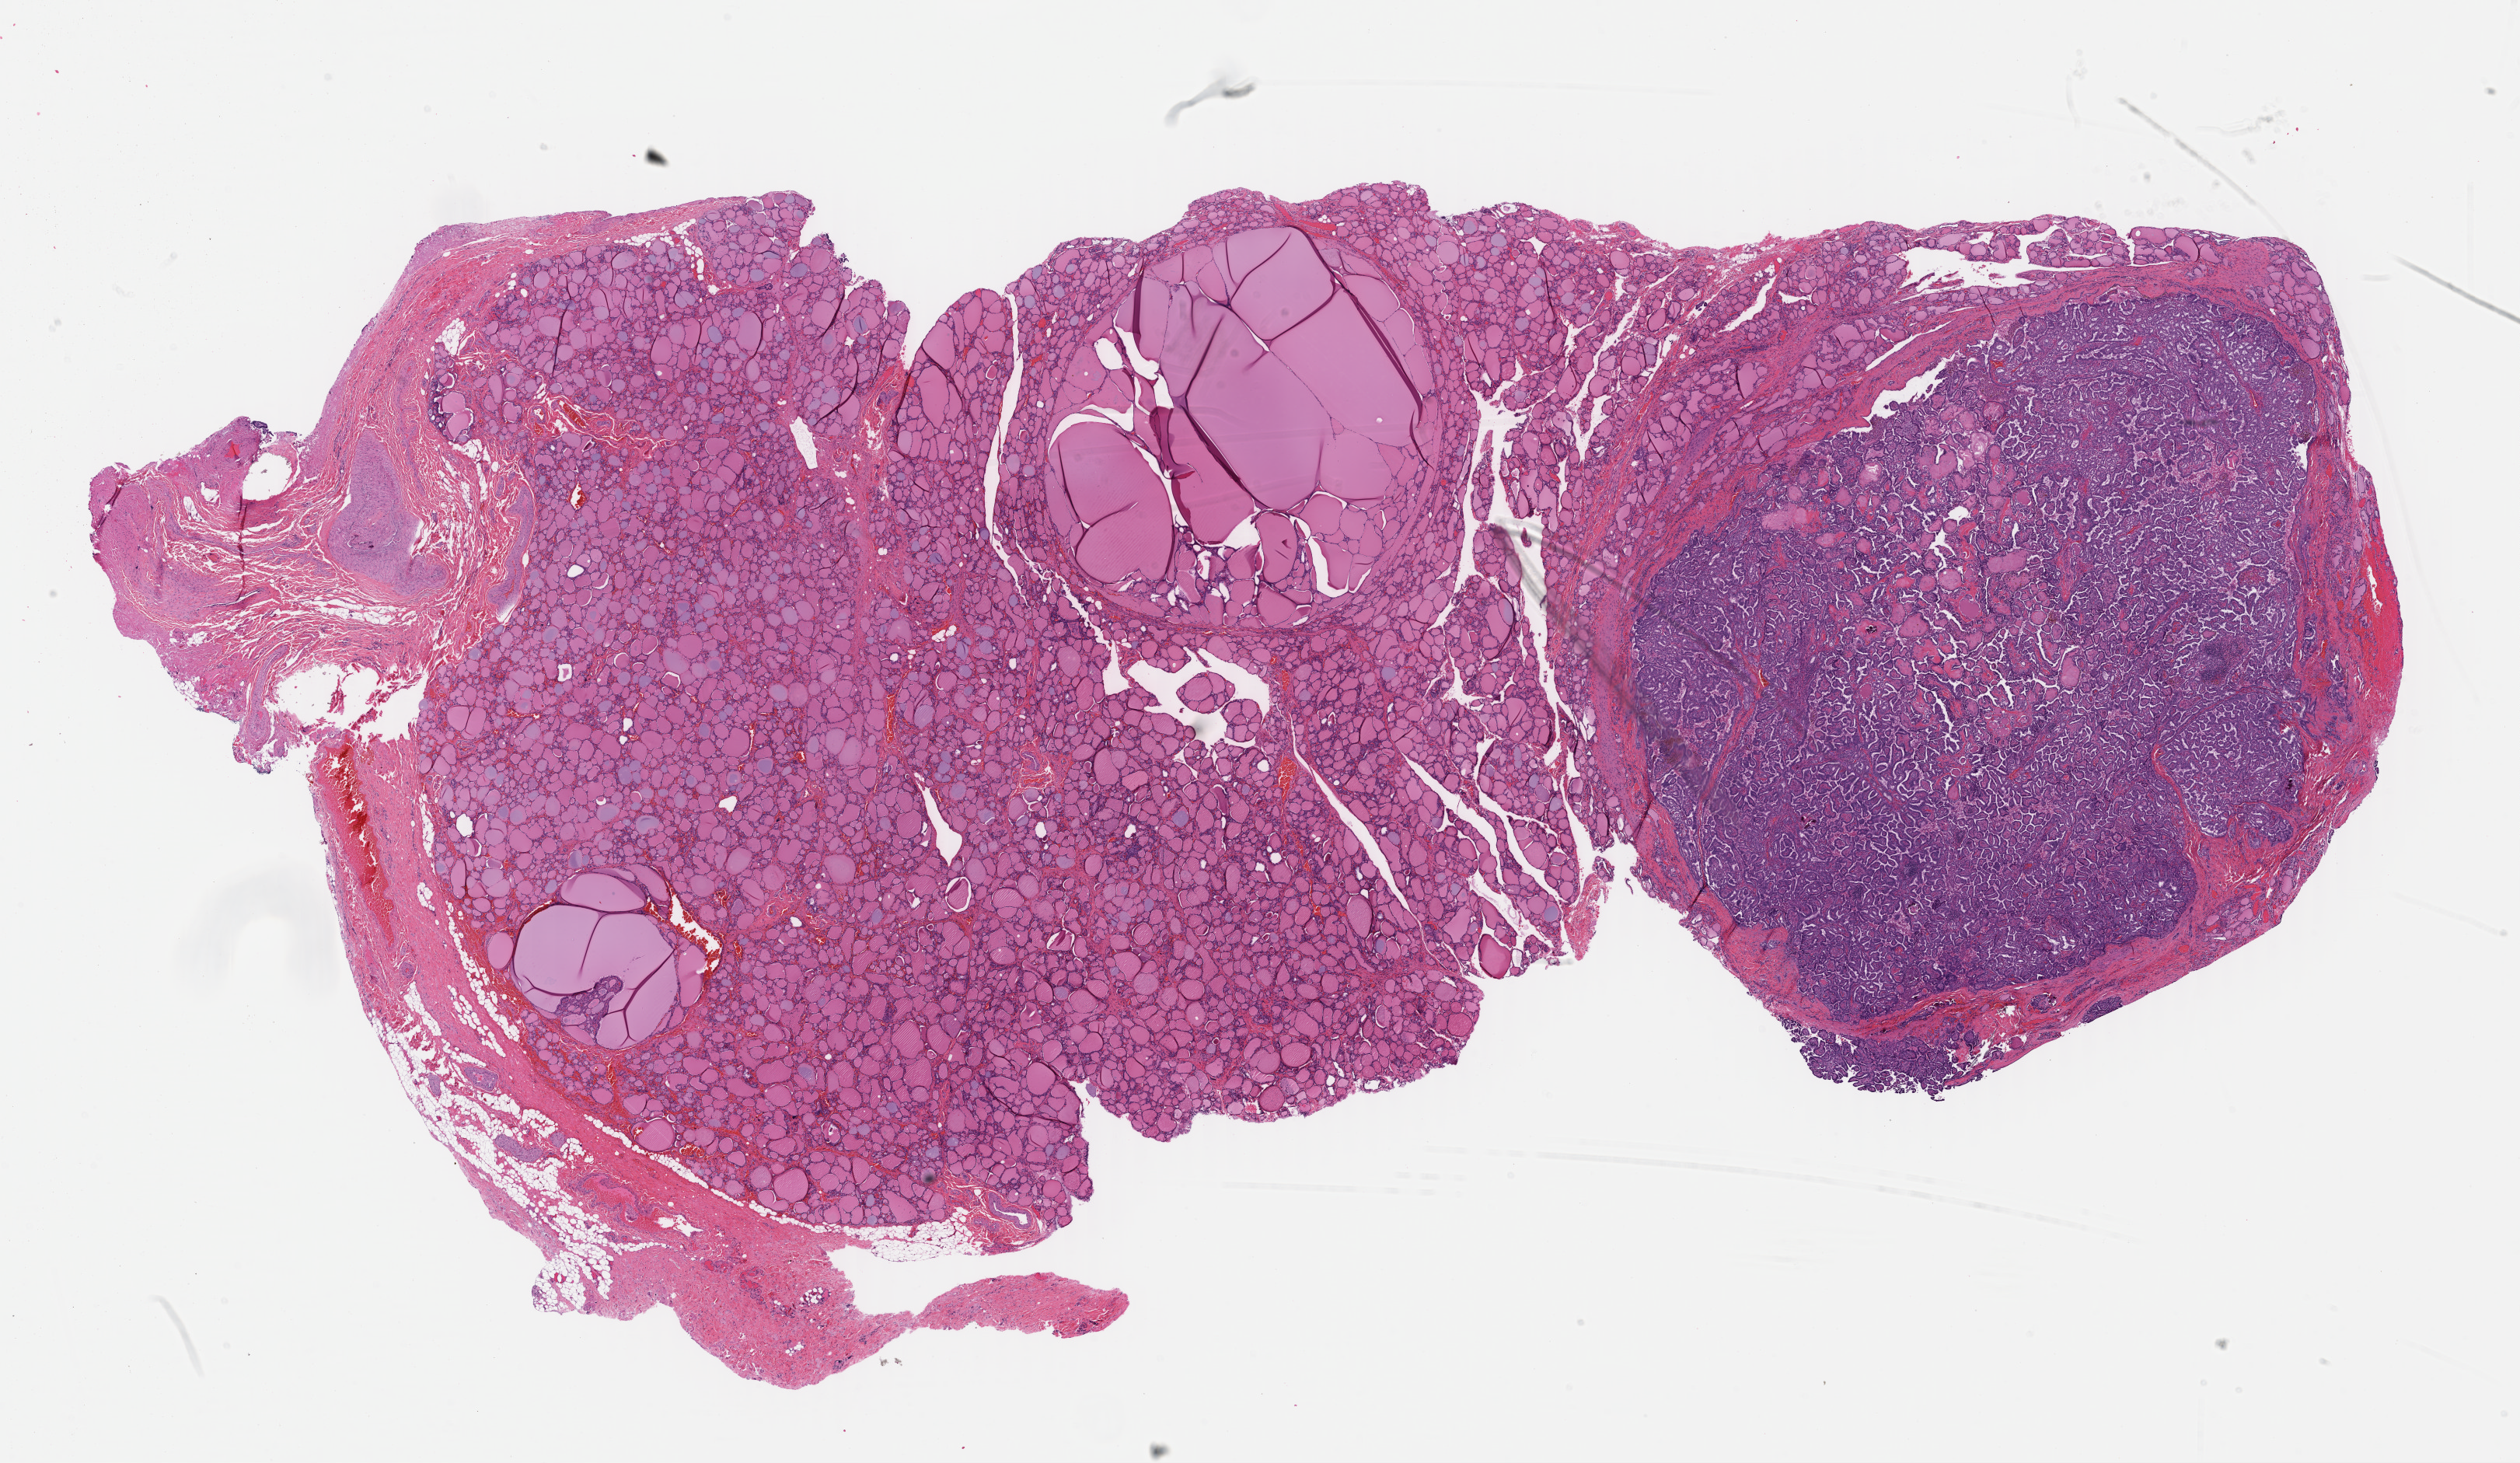
Whole-slide histology image, H&E-stained, low-resolution overview of the scanned area, about 25.5 x 14.8 mm (slide scanned at 40x); formalin-fixed paraffin-embedded (FFPE) diagnostic section; primary tumour sample from the thyroid. Female patient; age at initial diagnosis 54 years.
* AJCC pathologic stage: I (7th edition)
* histologic diagnosis: Papillary adenocarcinoma, NOS (thyroid gland)
* TNM: T1 N0 M0
* lymph nodes positive (case pathology): 0 of 1 examined